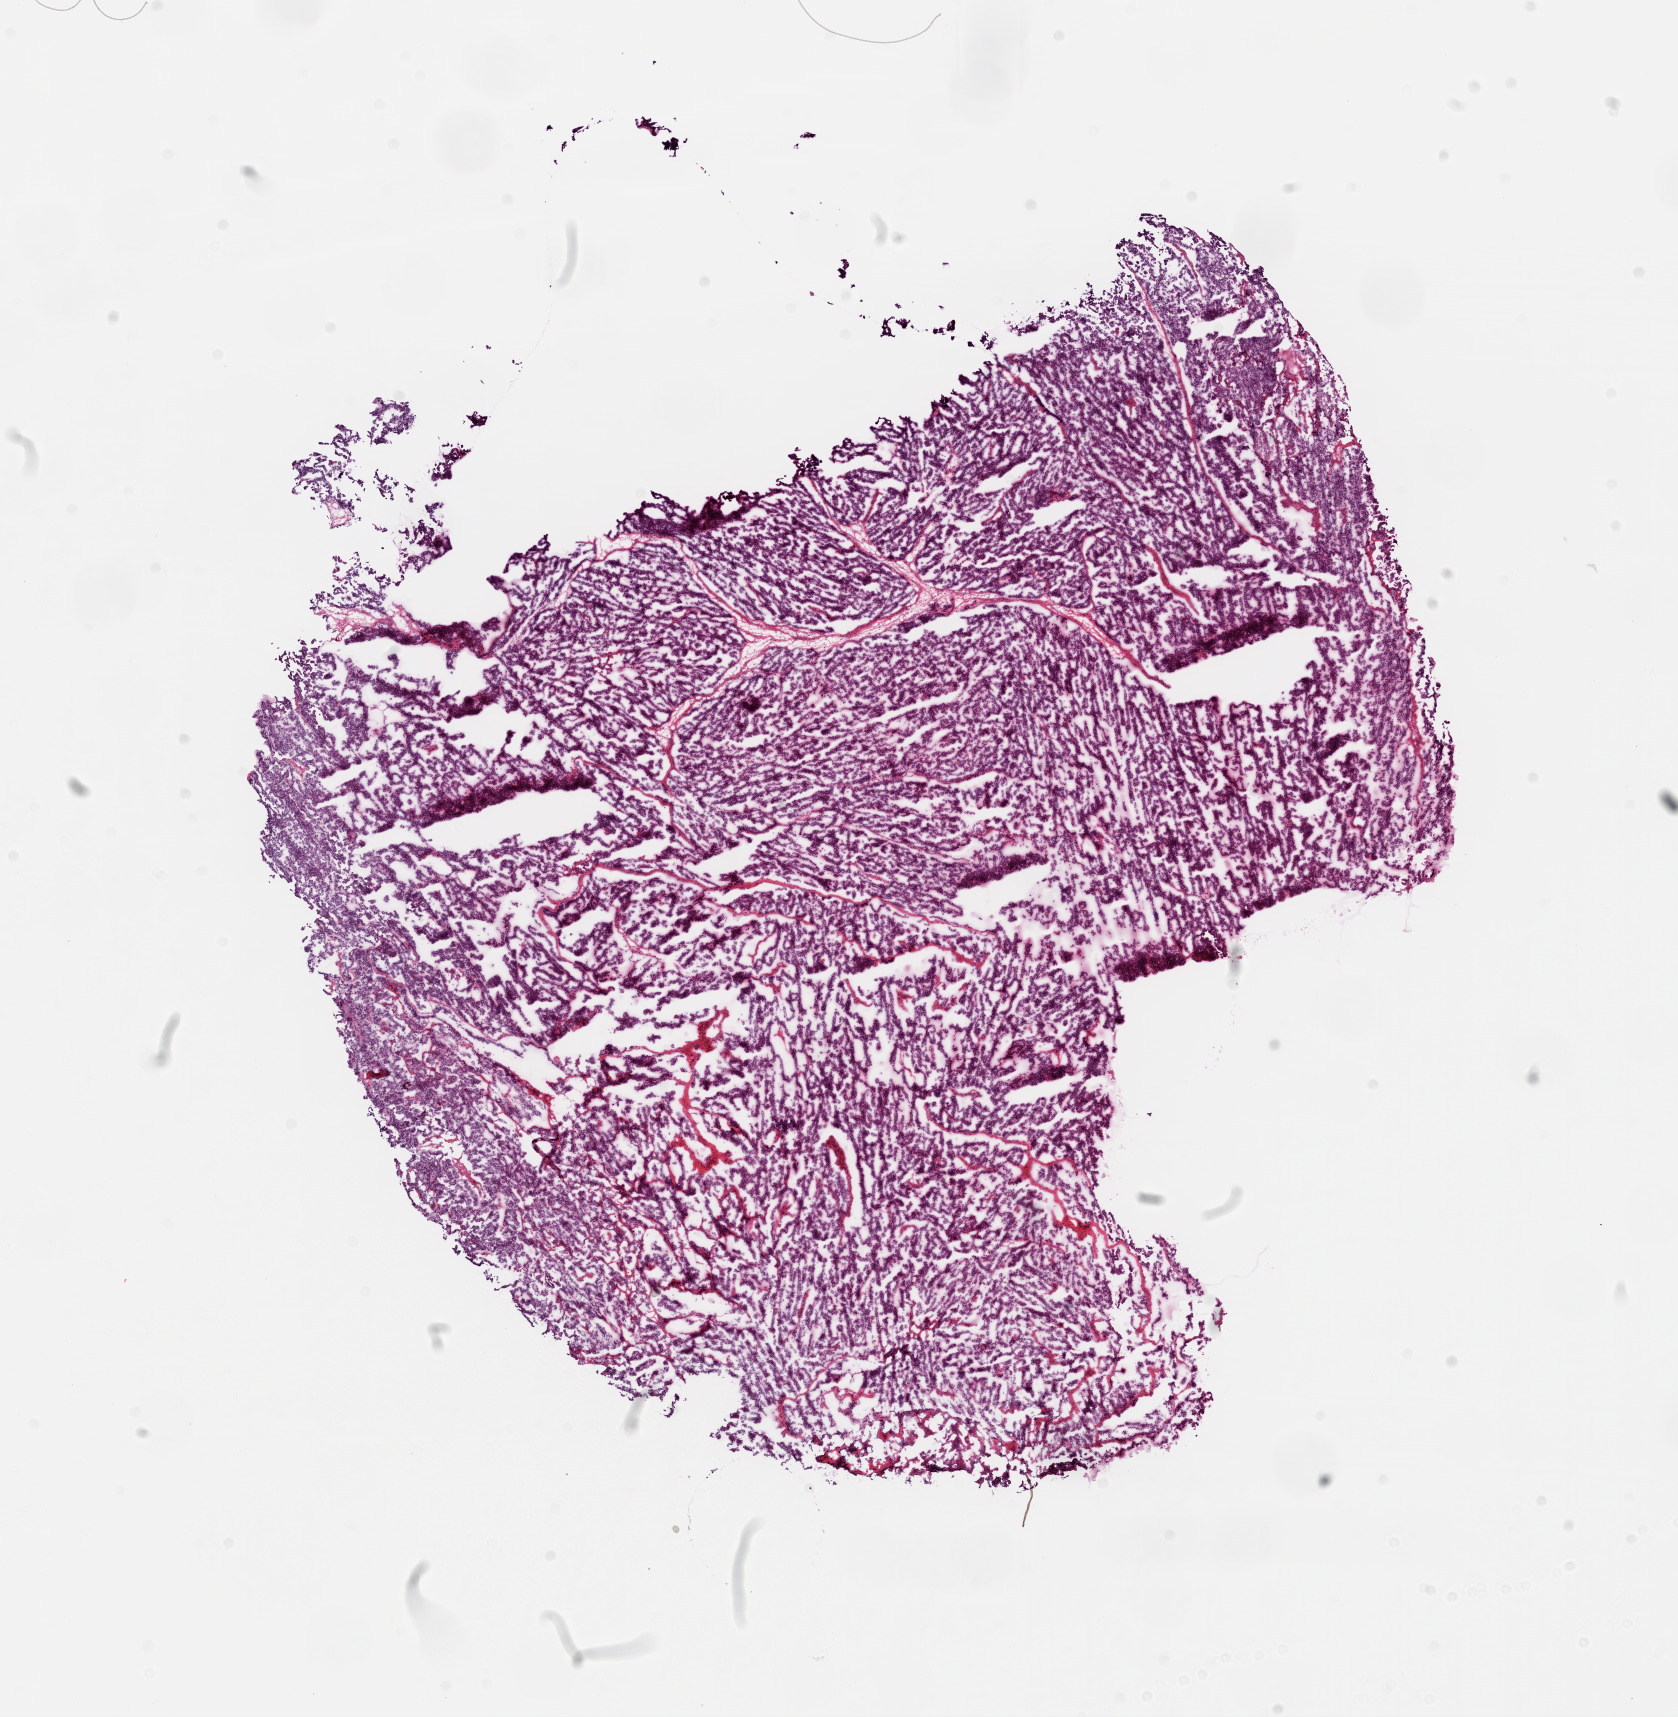
H&E whole-slide image — a low-resolution overview of the entire scanned area, about 13.5 x 13.9 mm; frozen section from the top of the tissue portion; sample: primary tumour, ovary. Female, age 44 years at initial diagnosis. Histologic grade: GX (grade cannot be assessed). Pathologist review of this section (percent, as recorded): tumour cells 95%, tumour nuclei 98%, normal cells 0%, stromal cells 5%, necrosis 0%.
FIGO stage: IIIC. Laterality: bilateral. Diagnosis: Serous cystadenocarcinoma, NOS.